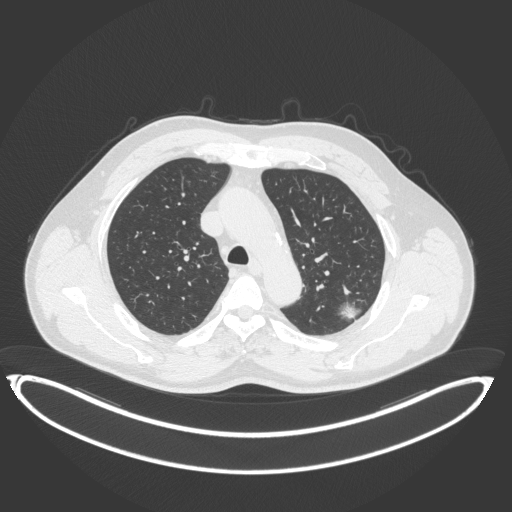
Chest CT, one axial slice; reconstruction kernel B31f; 120 kVp; lung window (W 1500 / L -600 HU); 512 × 512 image matrix, field of view 469 × 469 mm. Male patient, age 58 years. Case-level facts recorded for this patient, not image findings: clinical TNM (as recorded): T1c N0 M0.
Outlined on this slice (bounding box drawn by a radiologist):
- lung tumour (recorded histology: adenocarcinoma): bounding box [x1, y1, x2, y2] px = [334, 299, 365, 327]